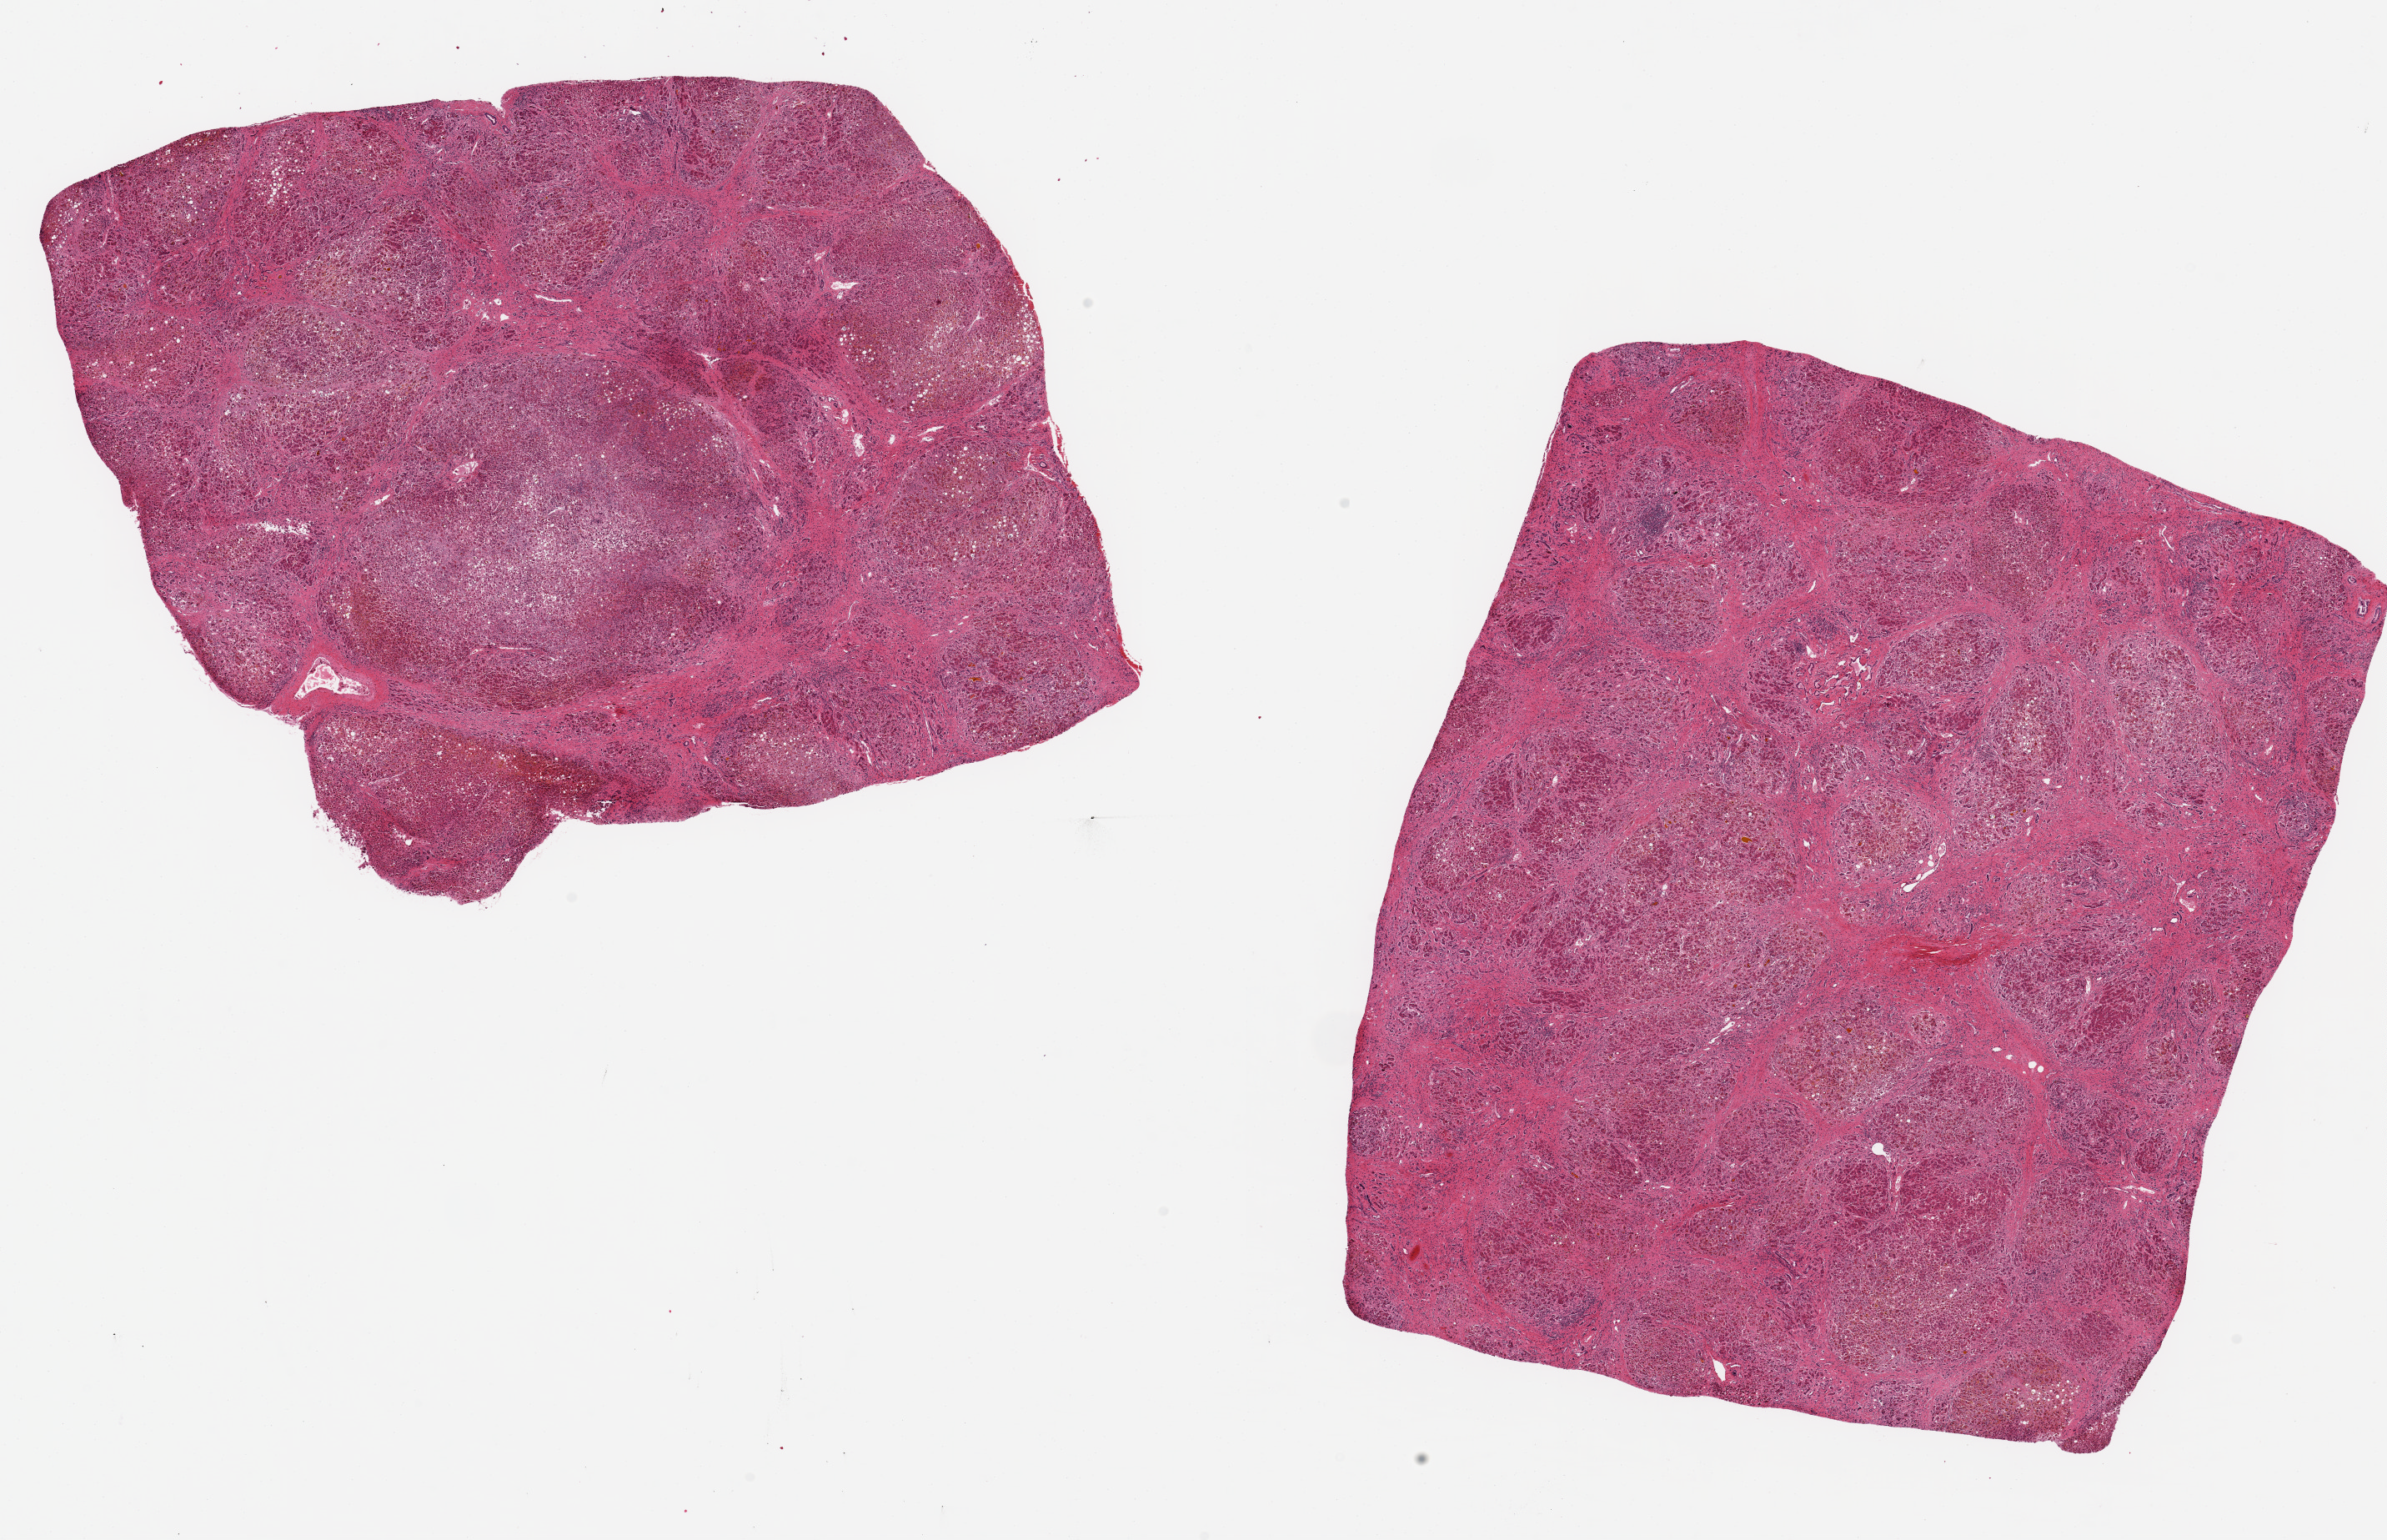
Haematoxylin and eosin whole-slide image, whole scanned area (about 22.6 x 14.6 mm, slide scanned at 20x) shown as a low-resolution overview, PAXgene-fixed paraffin-embedded (PFPE) section, sampled site (target tissue): liver, donor tissue sample. Male donor.
Pathologist's review note for this sample: 2 ~9x7mm aliquots. End-stage cirrhosis with marked bile stasis + steatosis.